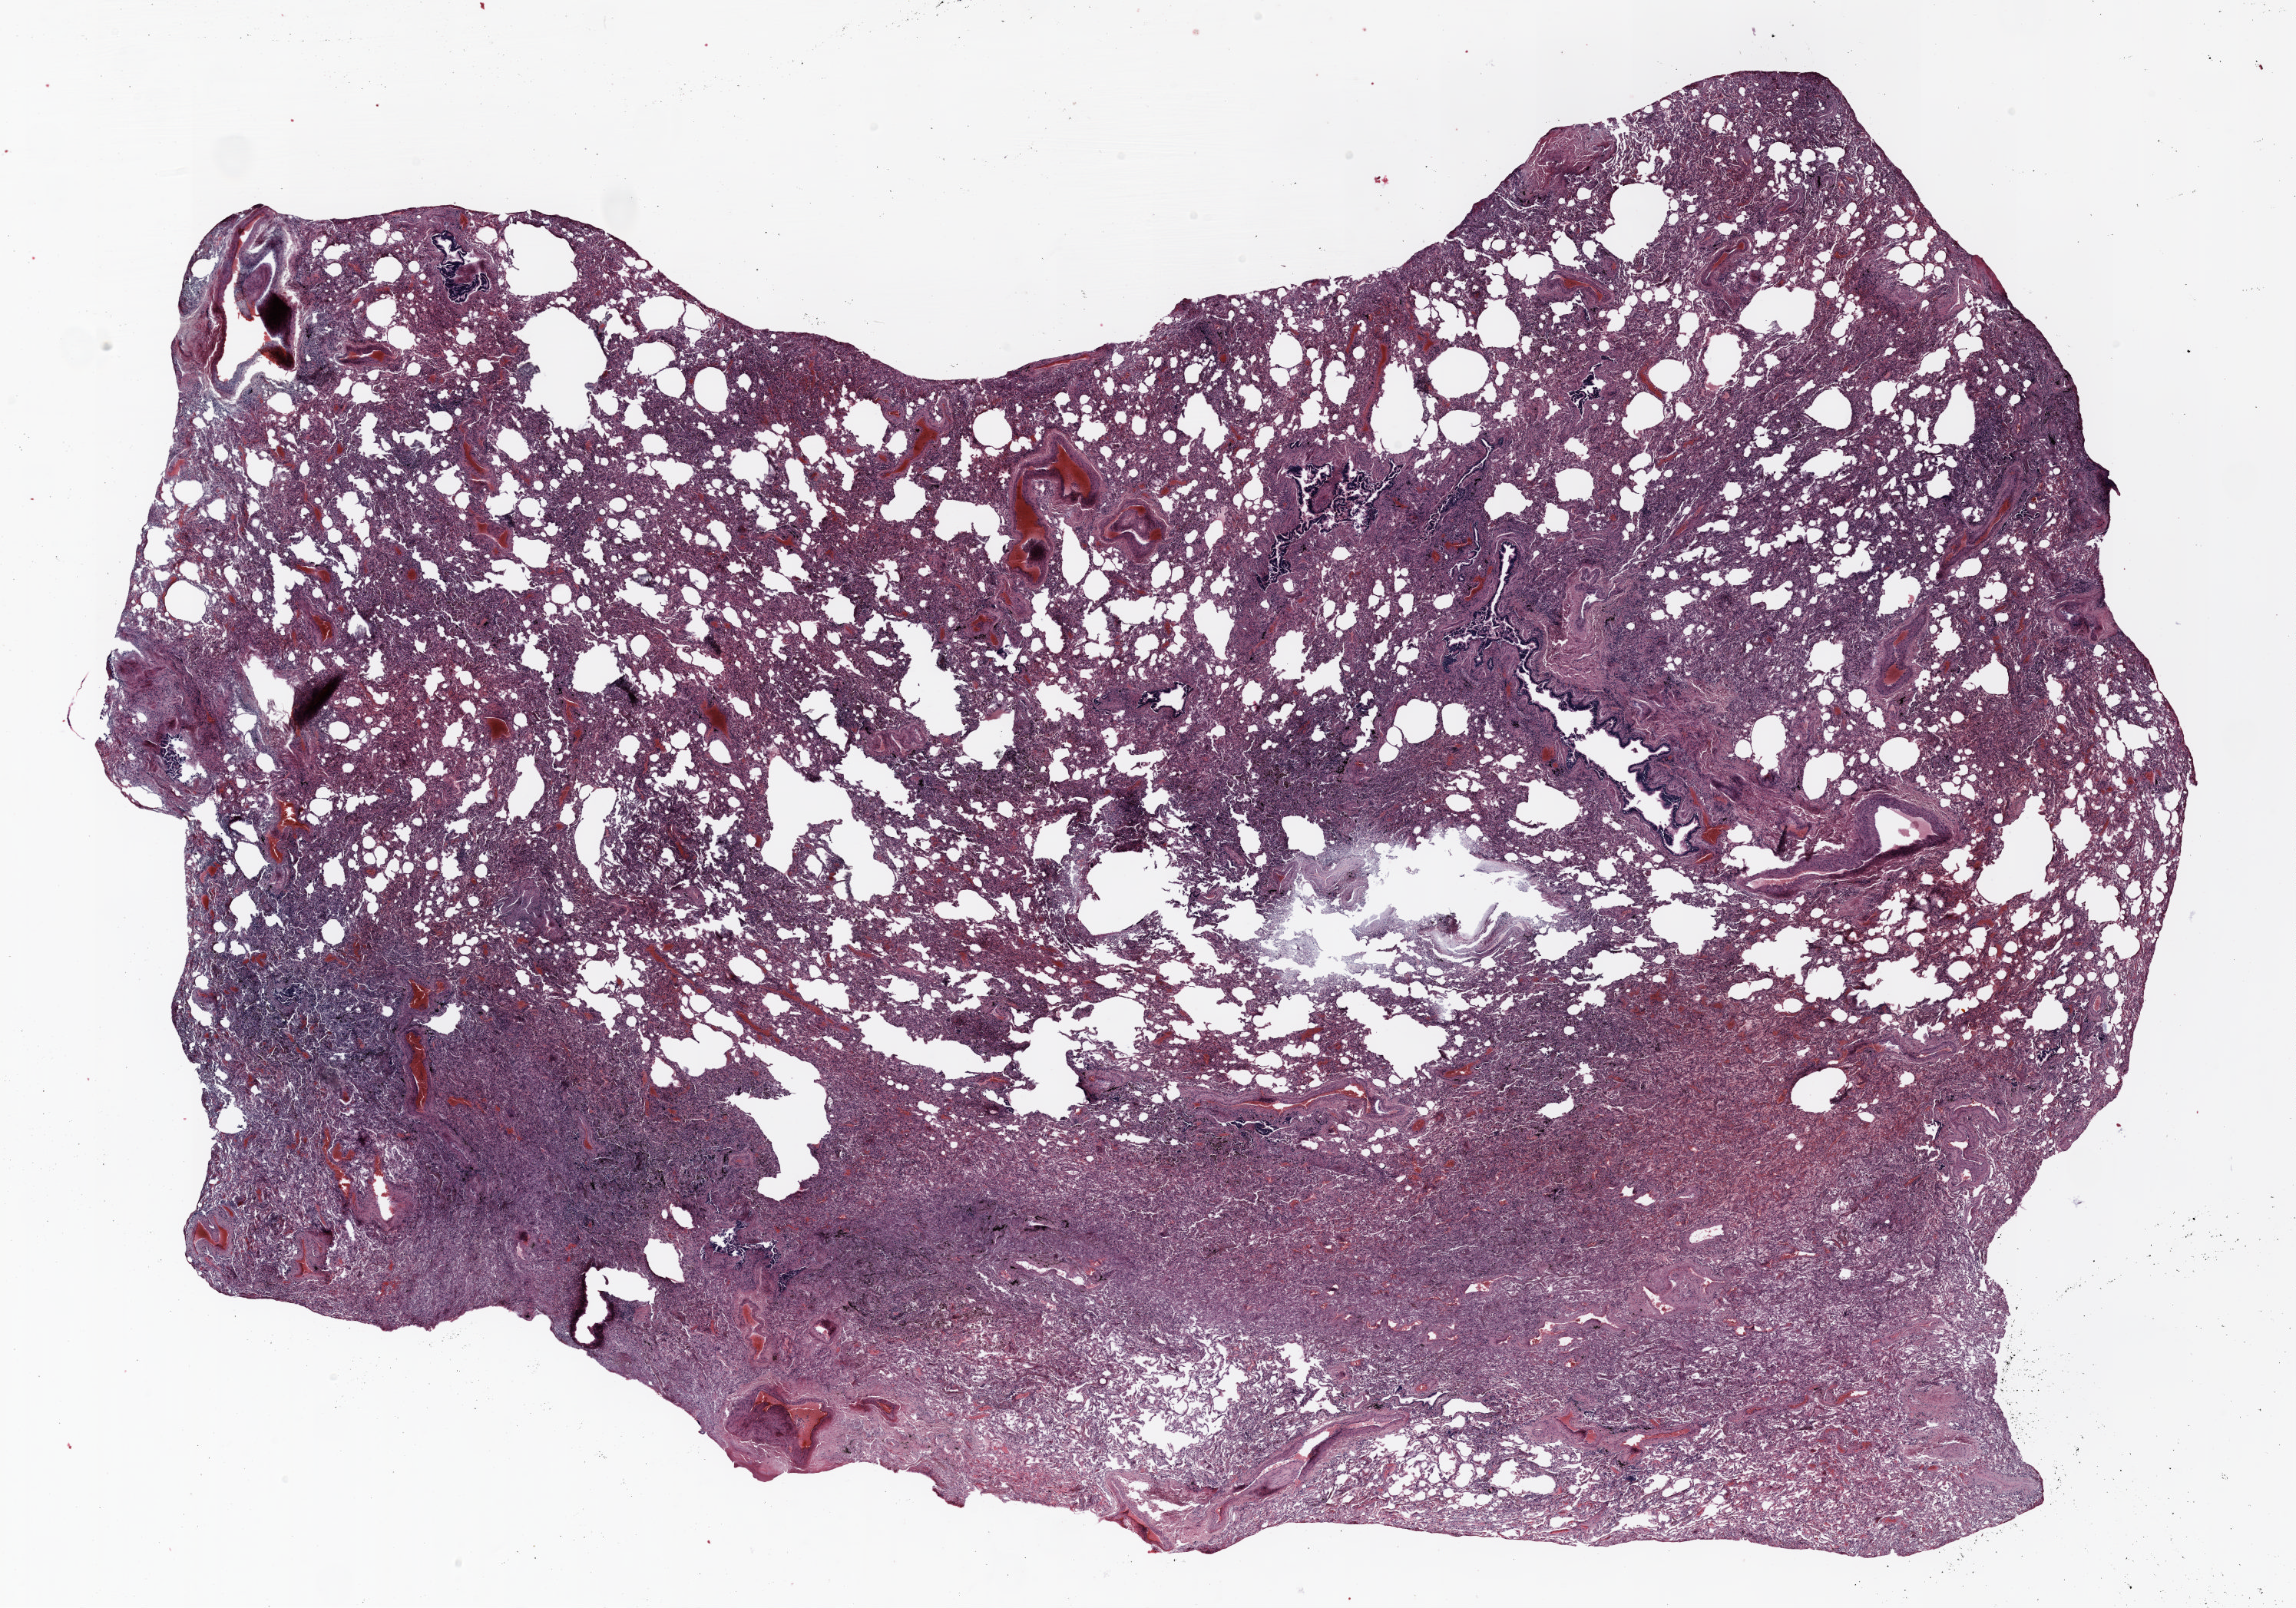
Hematoxylin and eosin (H&E) stained whole-slide image — a low-resolution overview of the entire scanned area, about 24.0 x 16.8 mm, formalin-fixed paraffin-embedded (FFPE) section, lung tissue. Male patient, aged 62 at enrolment. Current smoker at enrolment.
Participant's lung-cancer diagnosis: Bronchiolo-alveolar adenocarcinoma, NOS (ICD-O-3 8250/3).